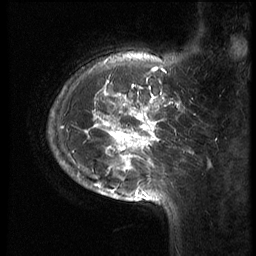
Breast MRI (dynamic contrast-enhanced), one sagittal slice; 3 images stored at this slice position (order not interpretable as contrast timing); 1.5 T; TE 4.2 ms, TR 9 ms; 256 × 256 image matrix, field of view 180 × 180 mm. Patient: female, 28 years. From the clinical record (not read from this slice): setting: breast cancer imaged before/during neoadjuvant chemotherapy.
Outlined on this slice (semi-automatically segmented with operator editing):
- analysis volume of interest (the breast-tissue region the enhancement analysis was run in; not a lesion): bounding box (x1, y1, x2, y2) in pixels: (46, 42, 186, 215)
- tumour enhancement mask (voxels above the 140 % enhancement threshold inside the analysis volume of interest): (63, 61, 176, 202)